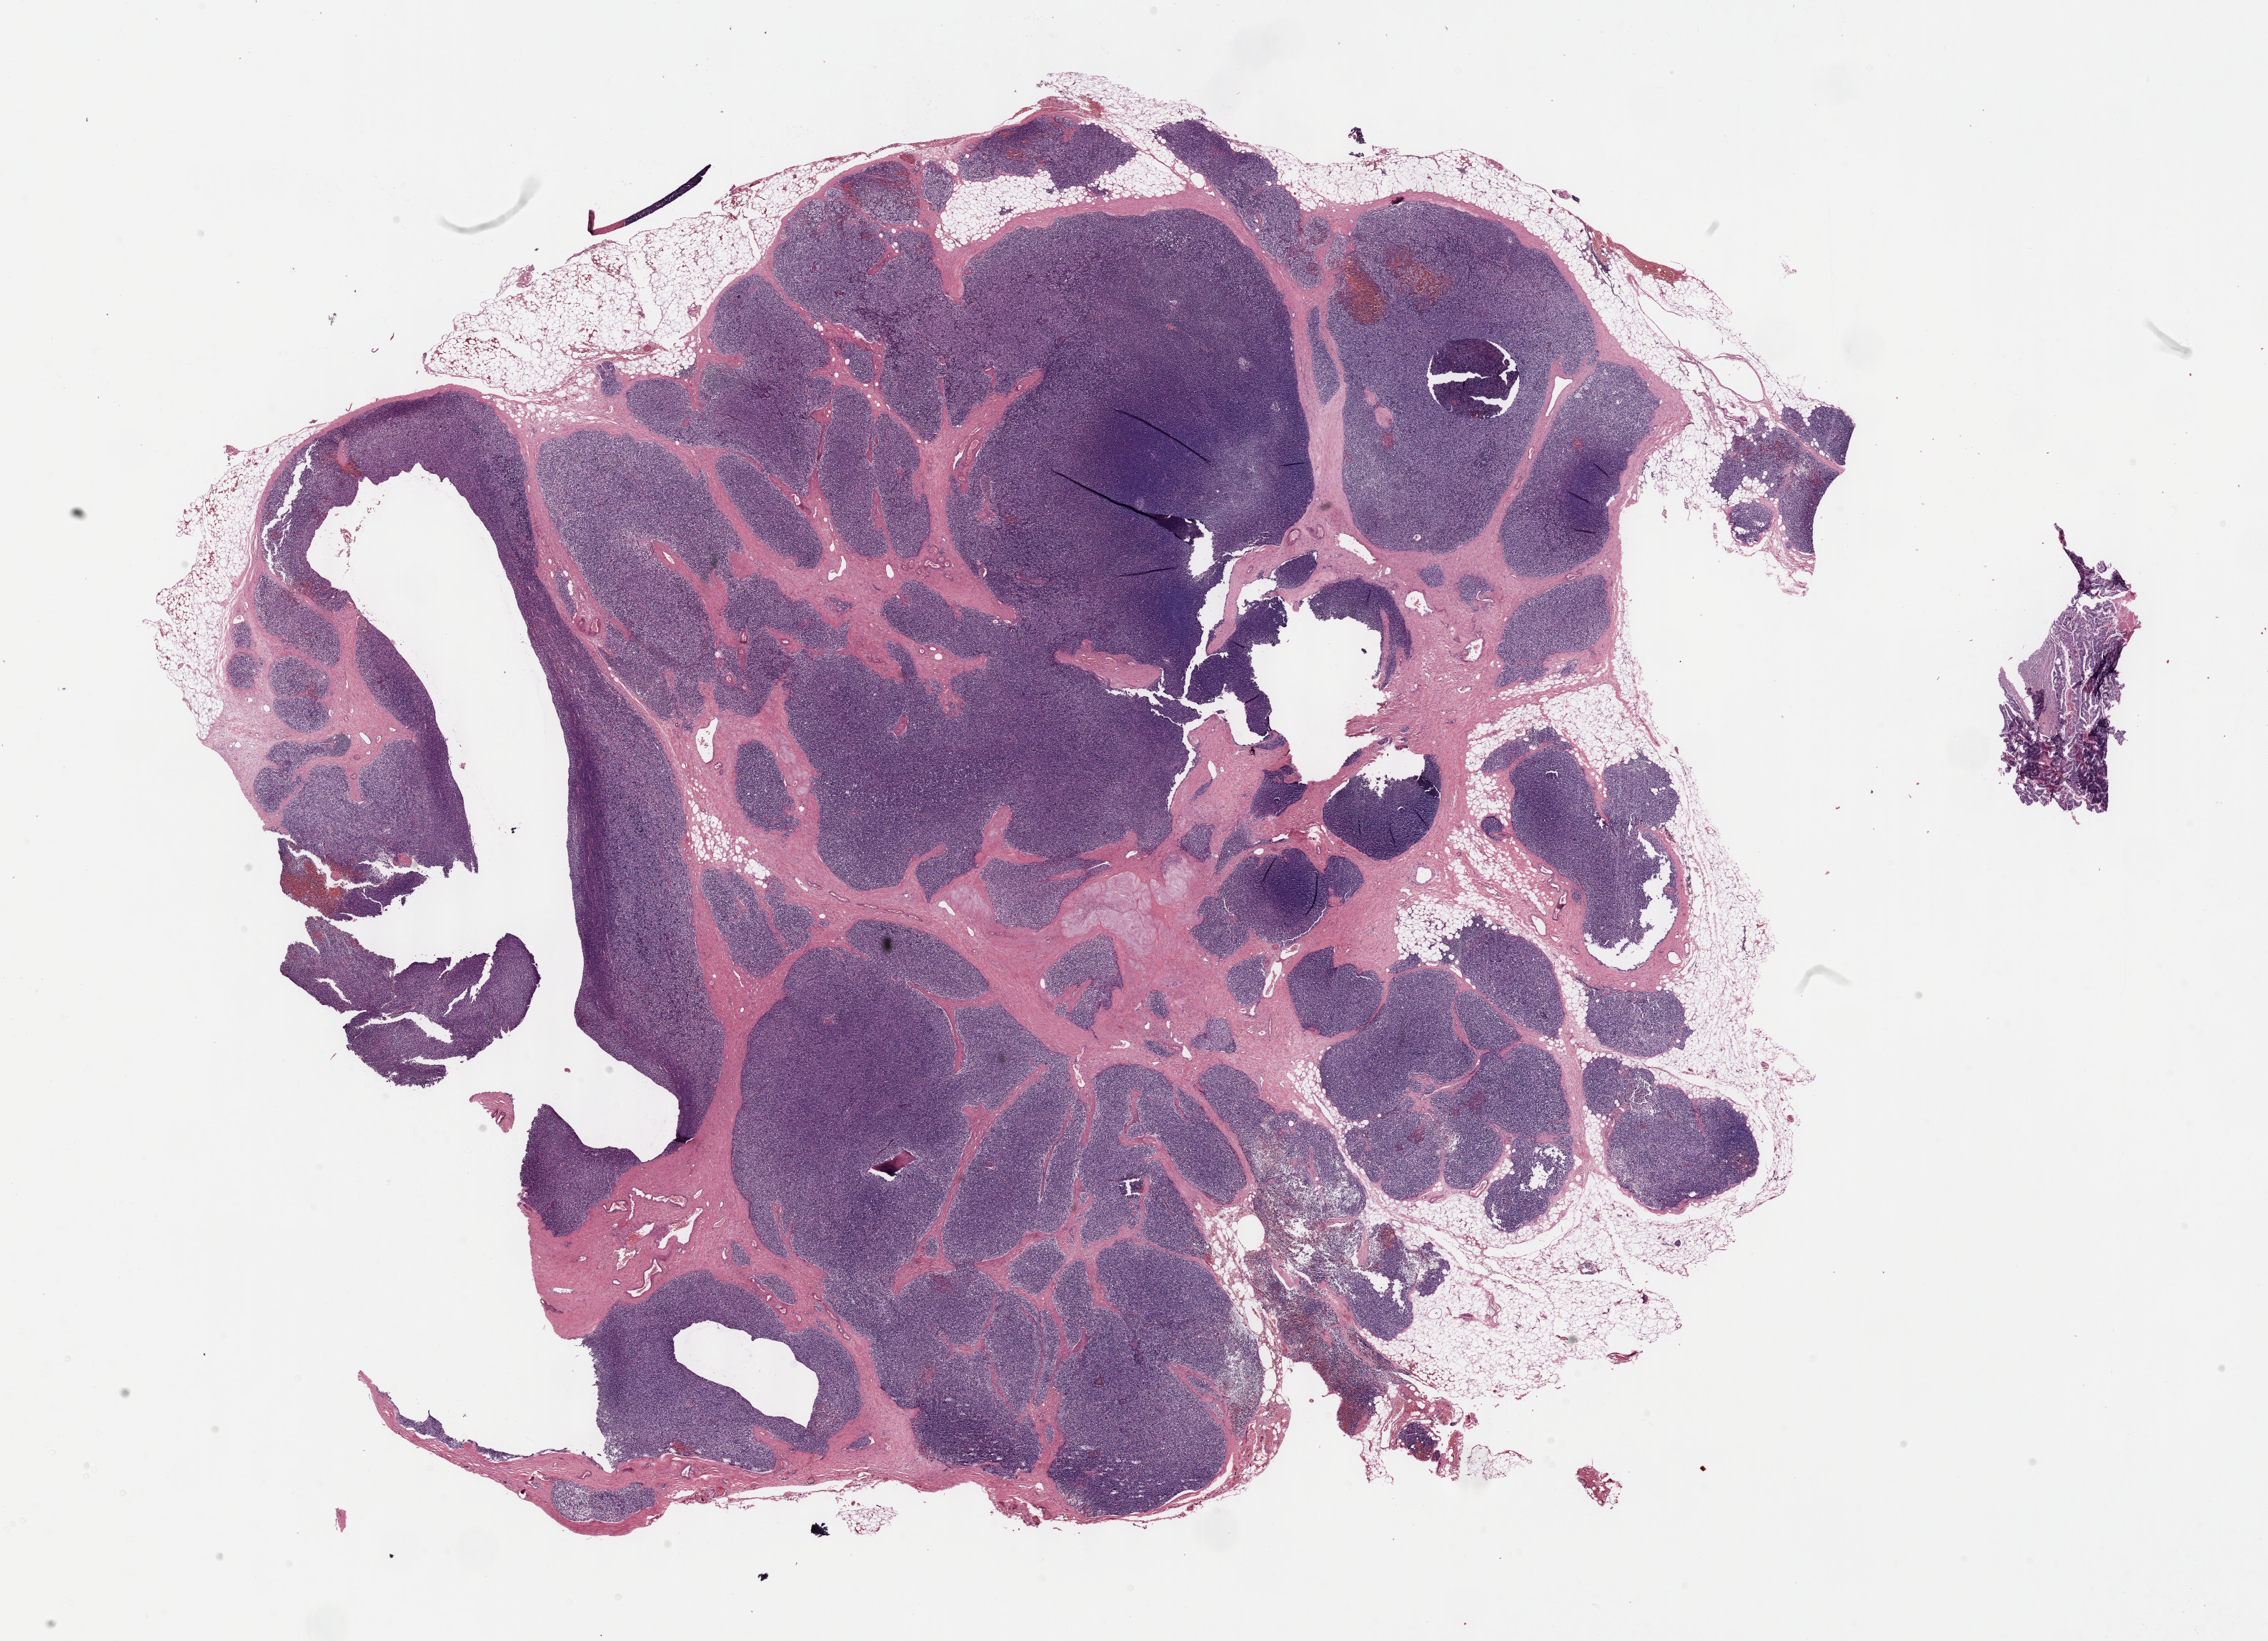
H&E-stained whole-slide image — whole scanned area (about 25.7 x 18.6 mm) shown as a low-resolution overview. FFPE section. Thymus, primary tumour sample. Patient: female, age at initial diagnosis 61 years.
- histologic diagnosis: Thymoma, type B2, NOS